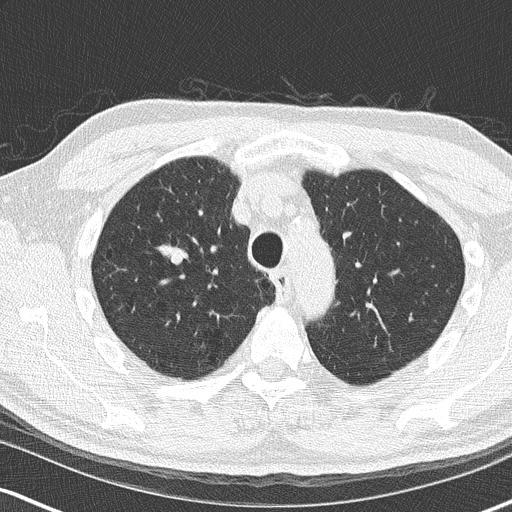
Axial slice from a low-dose chest CT screening exam, second screening round (one year after baseline), lung window (W 1500 / L -600 HU), 2 mm slice thickness, lung (sharp) reconstruction kernel (B50f), slice 52 of 170 in the series, 512 × 512 image matrix, field of view 320 × 320 mm. Male, age 68 years at enrolment. Current smoker at enrolment.
• Lesion marked by an expert reader, bounding box [x1, y1, x2, y2] px = [152, 231, 216, 292].
• Screening reader's record for this exam (one nodule recorded; not confirmed to be the boxed lesion): non-calcified nodule or mass ≥4 mm, right upper lobe, 18 × 15 mm, smooth margins, soft tissue attenuation, pre-existing on the prior screen: no.
• Official screen result: positive, change unspecified: nodule(s) >= 4 mm or enlarging nodule(s), mass(es), or other non-specific abnormalities suspicious for lung cancer.
• Participant outcome: lung cancer diagnosed 136 days after this screen — small cell carcinoma, NOS, right upper lobe, stage IIIB (AJCC 6th edition), 20 mm at pathology.